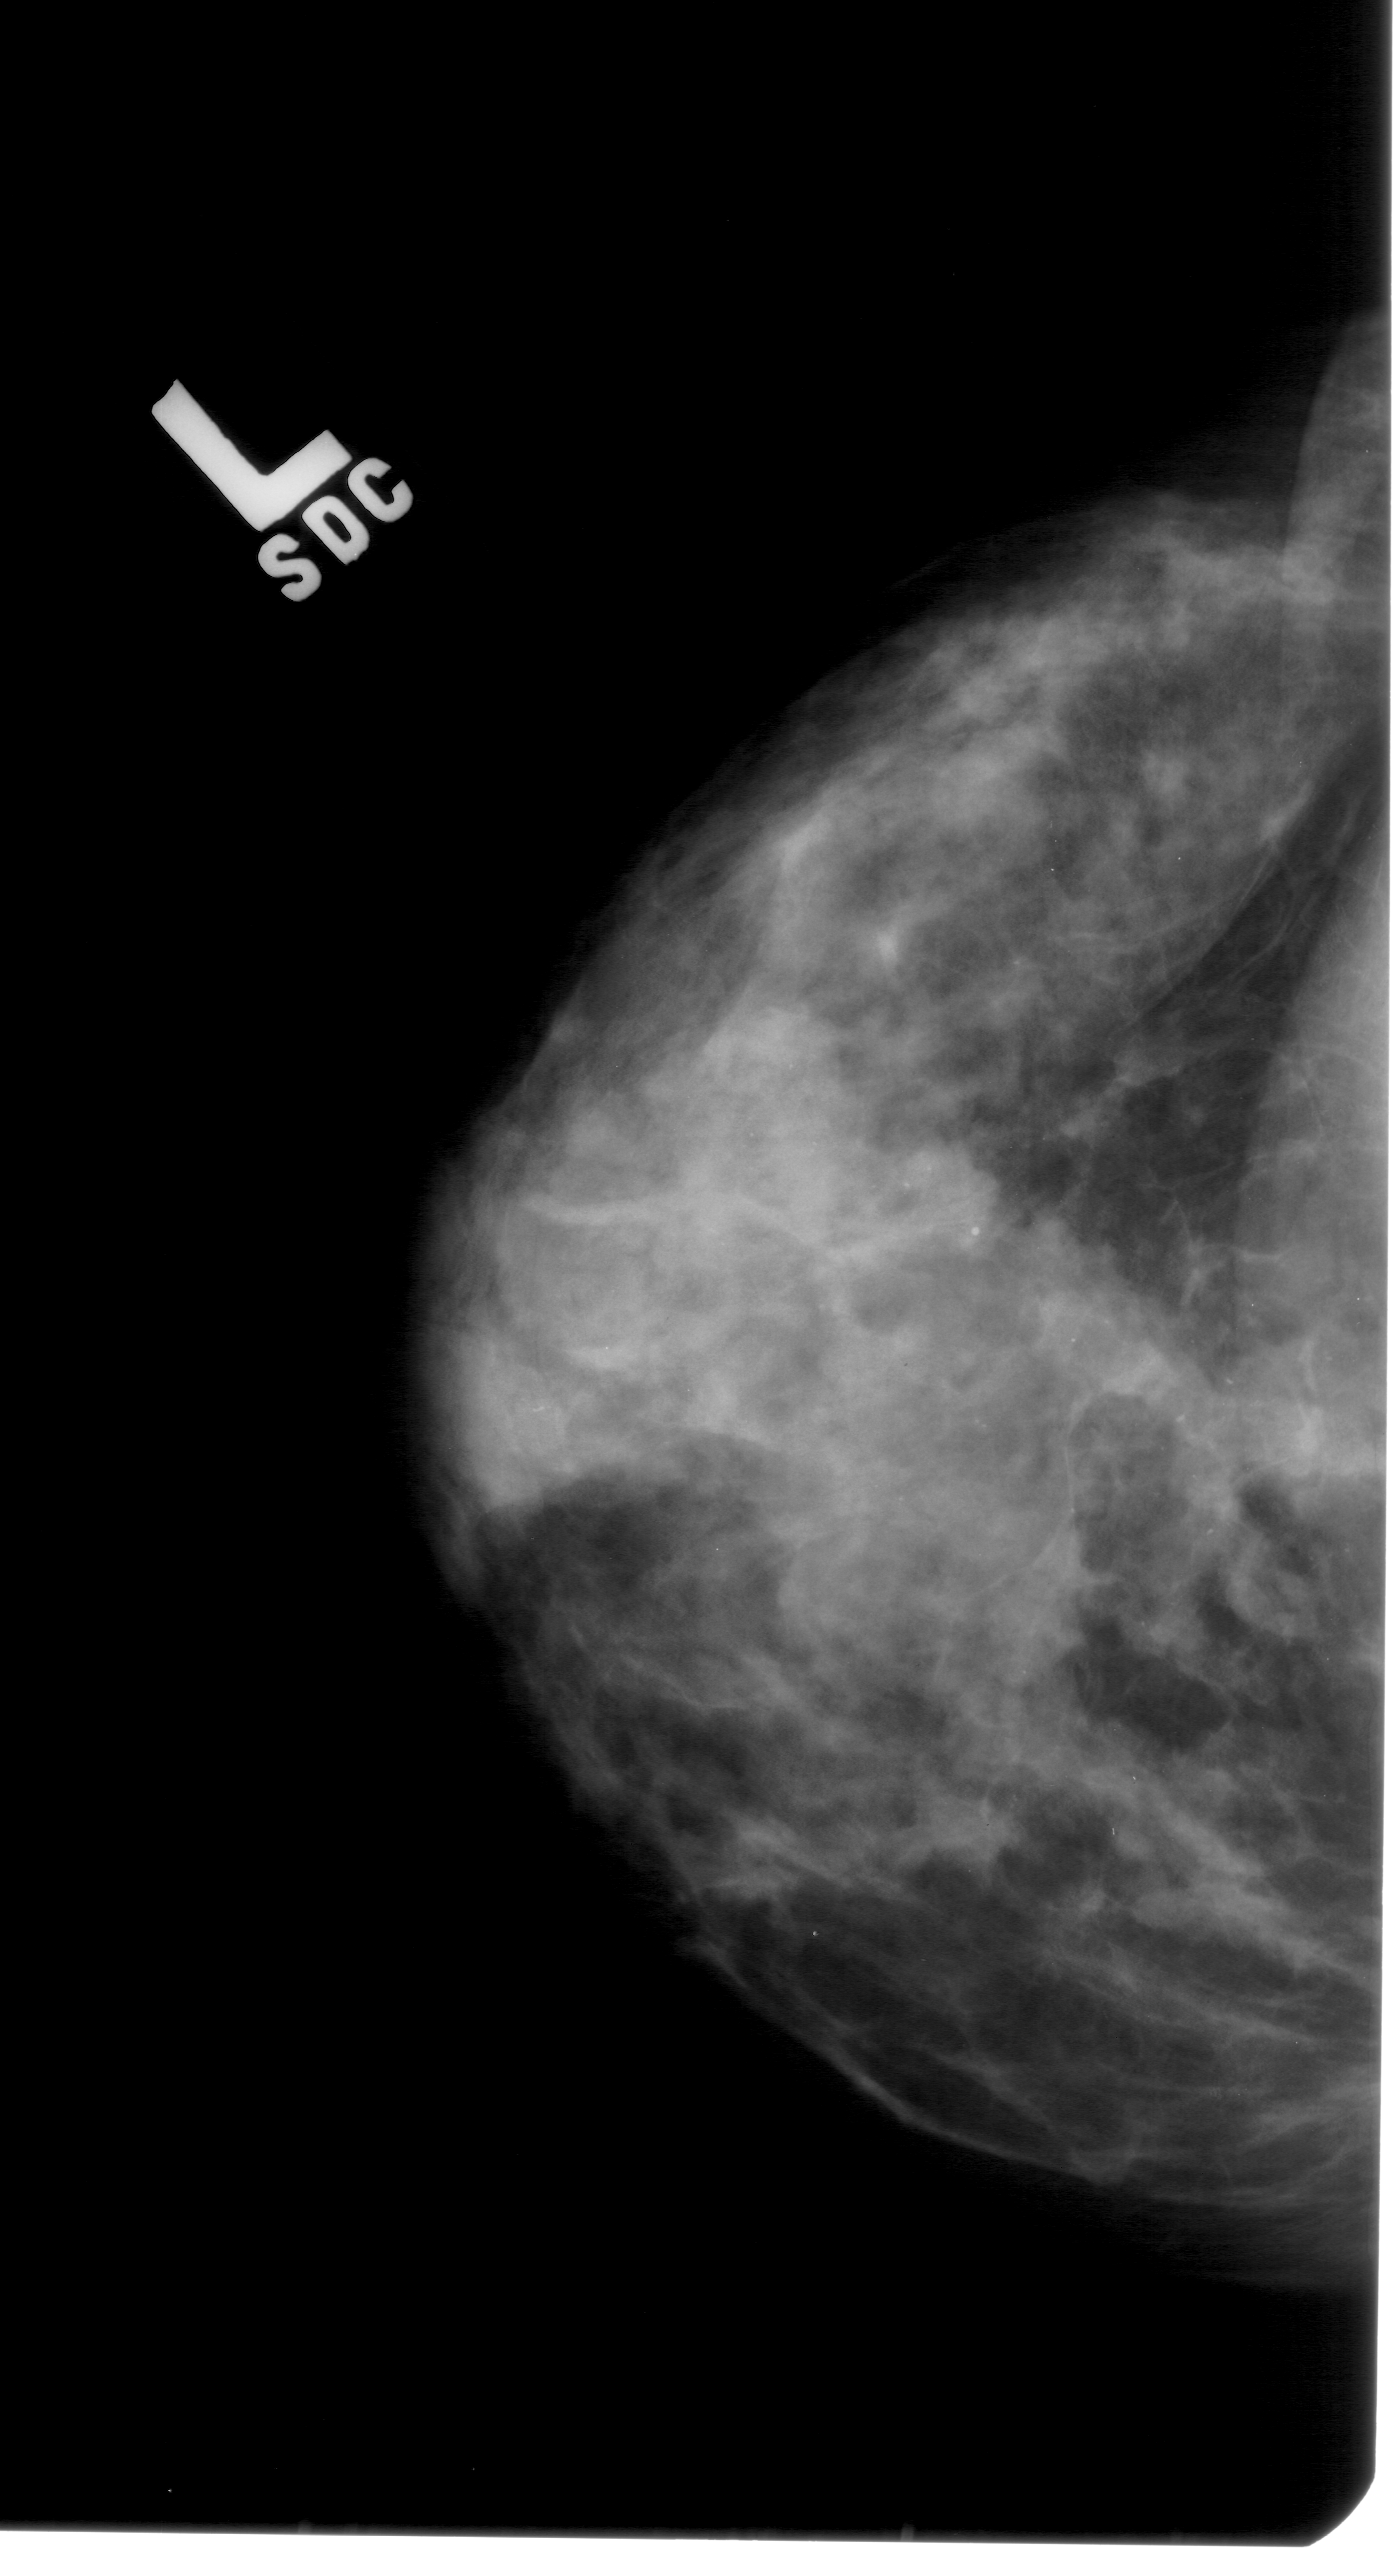
Digitized screen-film mammogram; left breast; craniocaudal (CC) view.
Finding: calcifications, morphology pleomorphic, distribution segmental; BI-RADS assessment category 4; subtlety rating 3 on a 1 (subtle) to 5 (obvious) scale; pathology (as recorded): malignant.